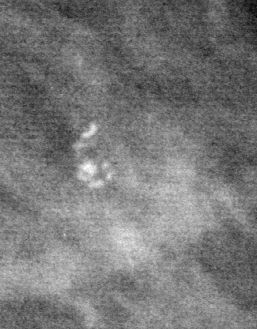
Cropped region of a digitized screen-film mammogram centred on a radiologist-marked abnormality; left breast; MLO view; BI-RADS breast density category 1 (scale 1–4).
Marked abnormality: calcifications, morphology pleomorphic, distribution clustered; BI-RADS assessment category 4; subtlety rating 4 on a 1 (subtle) to 5 (obvious) scale; pathology (as recorded): benign.